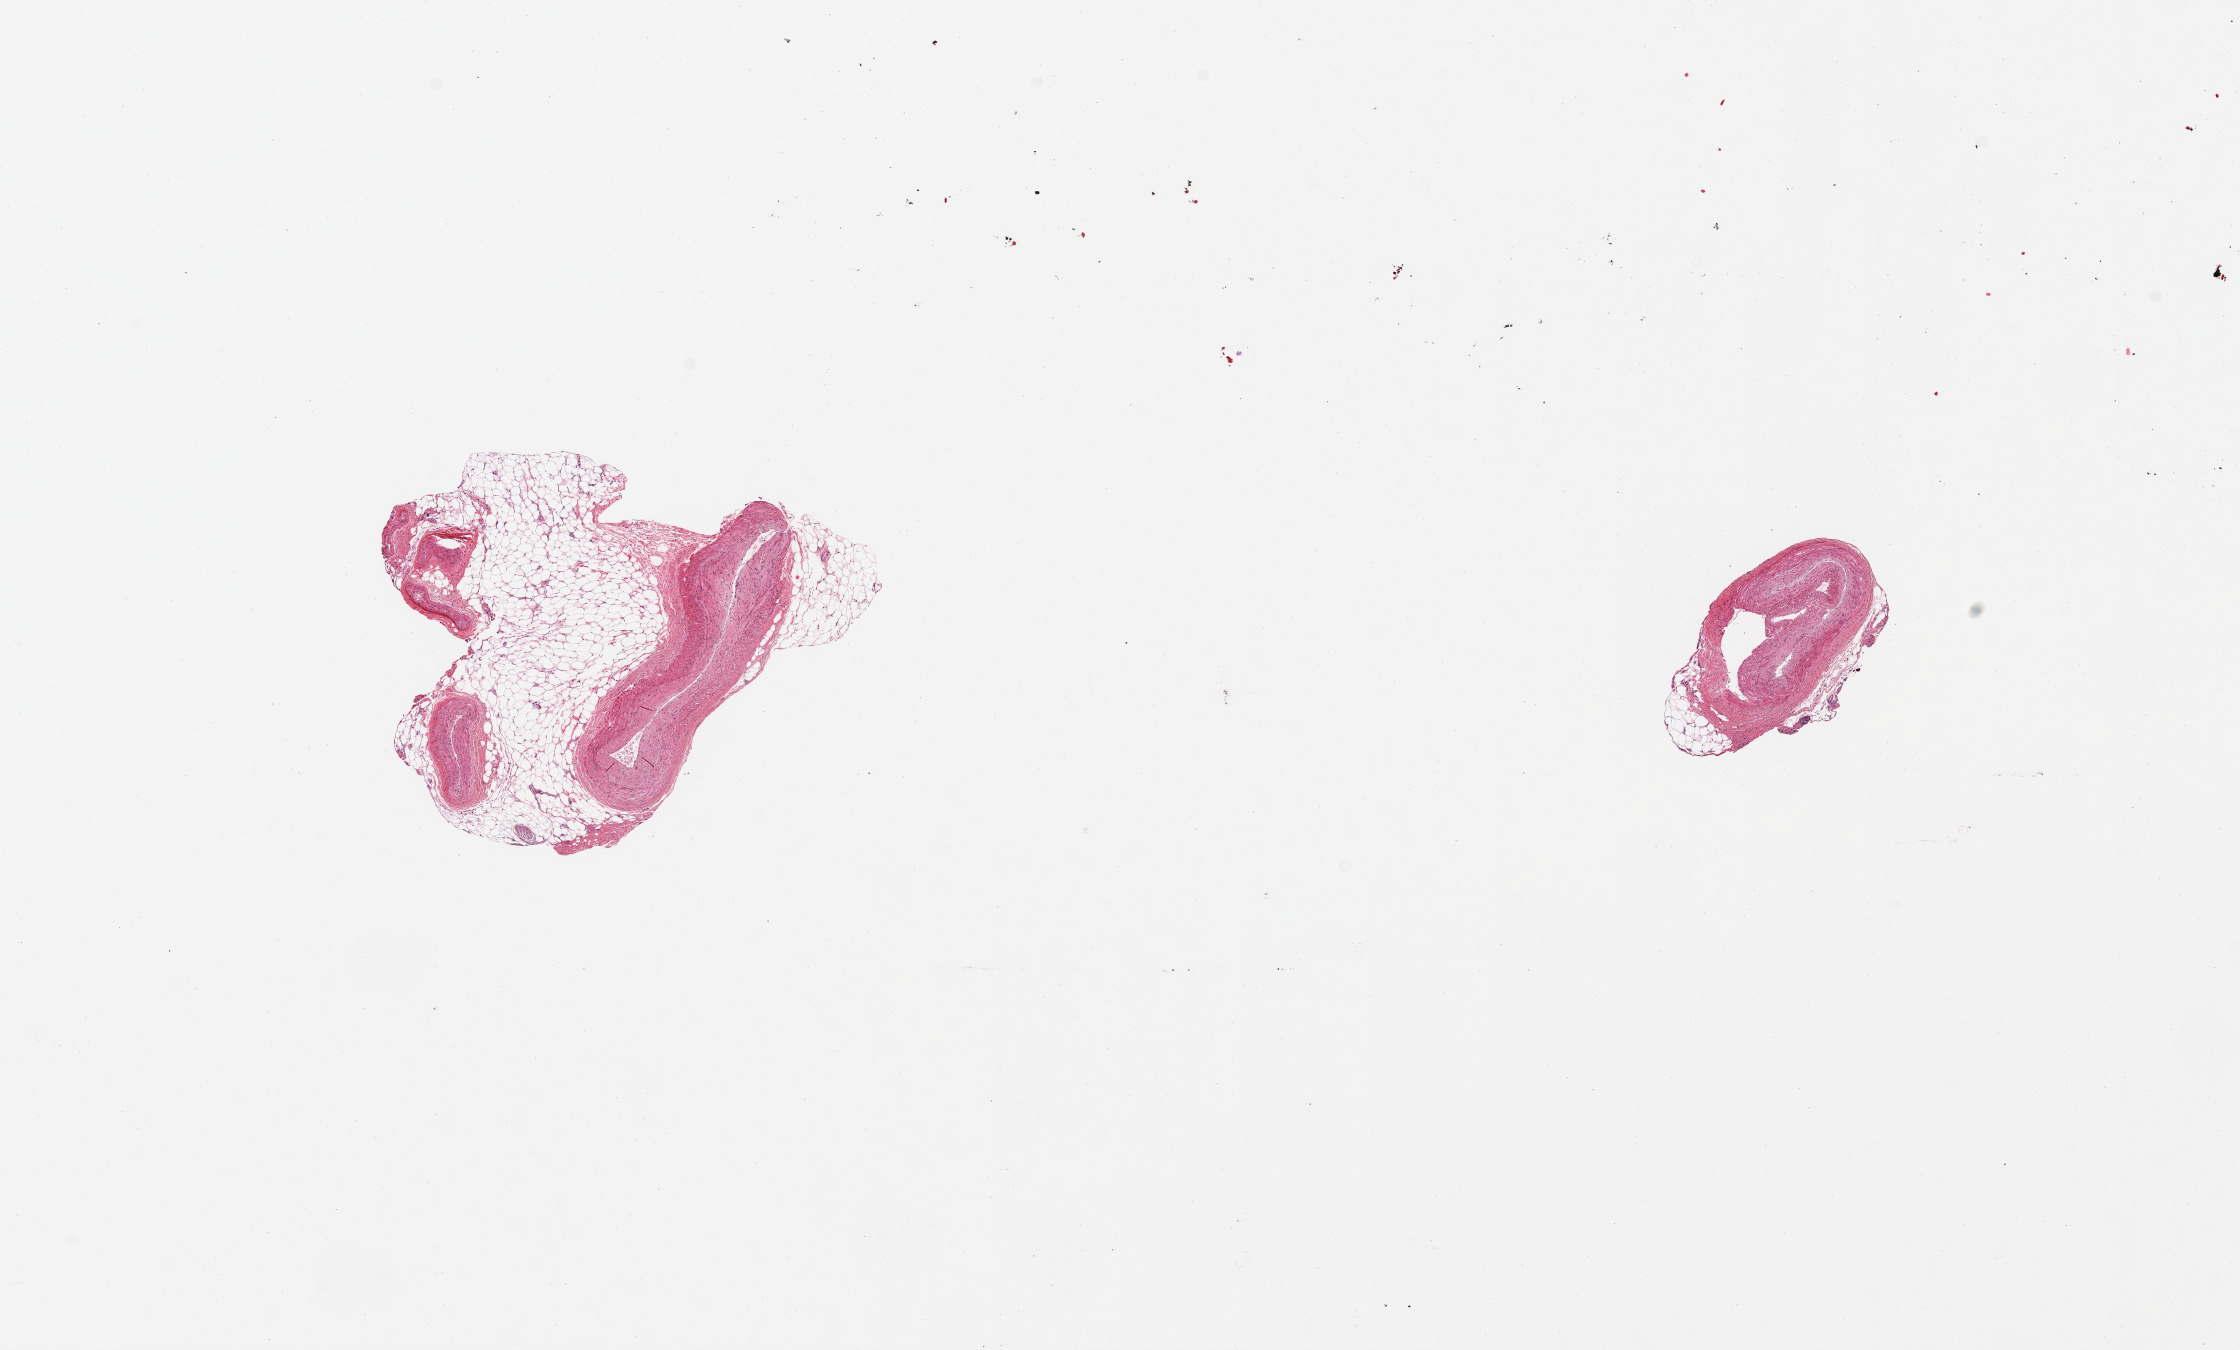
Whole-slide image, haematoxylin and eosin stain — low-resolution overview of the scanned area, about 17.7 x 10.7 mm (slide scanned at 20x); PAXgene-fixed, paraffin-embedded tissue; target tissue: coronary artery; donor tissue sample. Donor sex: male.
Review note (as recorded): 2 pieces; one piece is ~70% fat/vein/nerve.